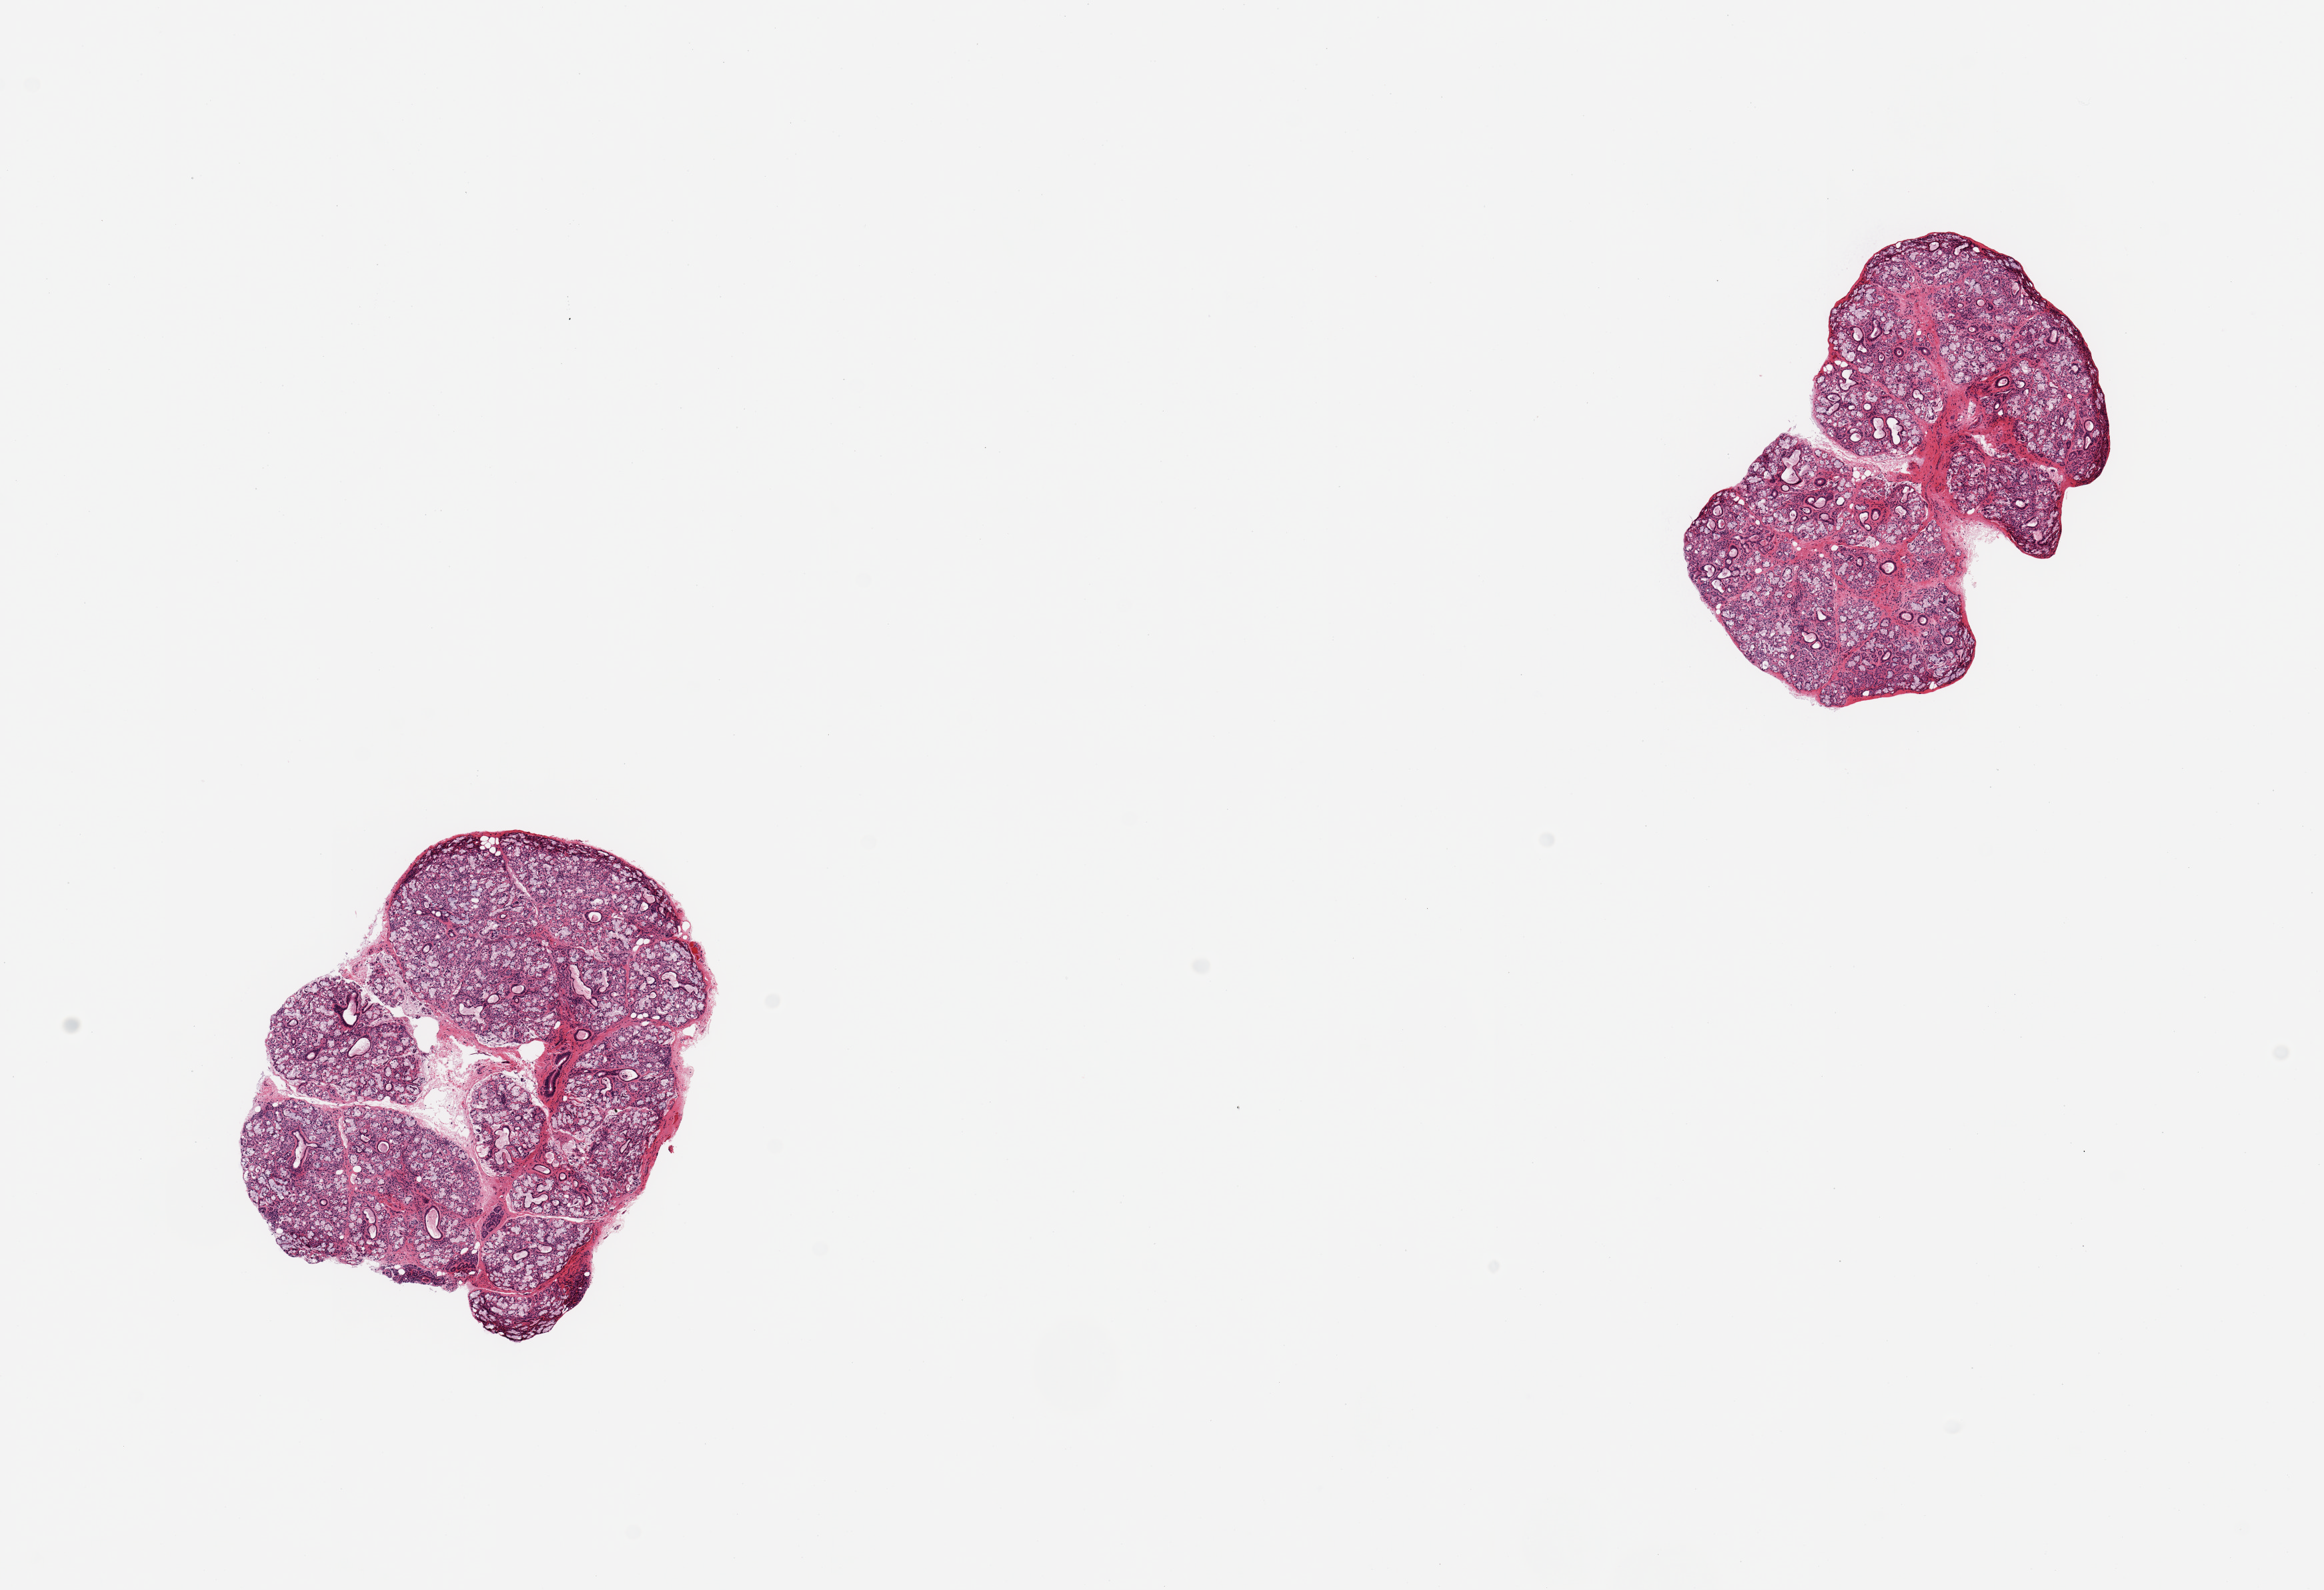
Digitized H&E-stained section, low-resolution overview of the scanned area, about 13.8 x 9.4 mm (from a 20x scan). PAXgene-fixed paraffin-embedded (PFPE) section. Sampled site (target tissue): minor salivary gland. Donor tissue sample. Donor sex: male.
Pathologist's review note for this sample: 2 pieces, all glandular parenchyma, excellent specimens.